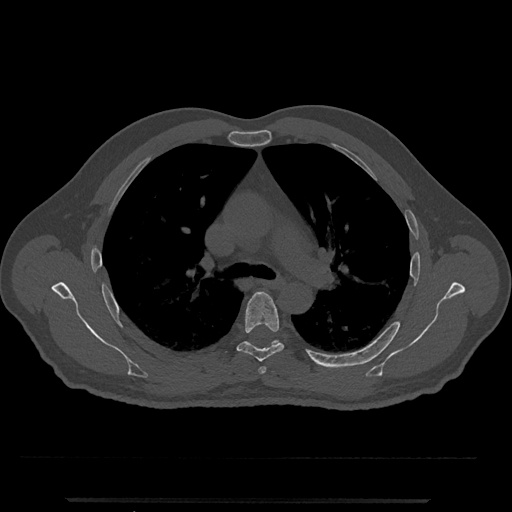
CT including the spine, one axial slice; position 789 of 797 along the scan axis; 120 kVp; bone window (W 1800 / L 400 HU); 512 × 512 image matrix. Patient: male, 63 years. From the clinical record (not read from this slice): primary cancer: prostate.
Outlined on this slice (semi-automatic segmentation, software-assisted and operator-edited):
- T5 vertebra: bounding box (x1, y1, x2, y2) in pixels: (237, 291, 284, 362)
- T6 vertebra: (271, 340, 281, 346)